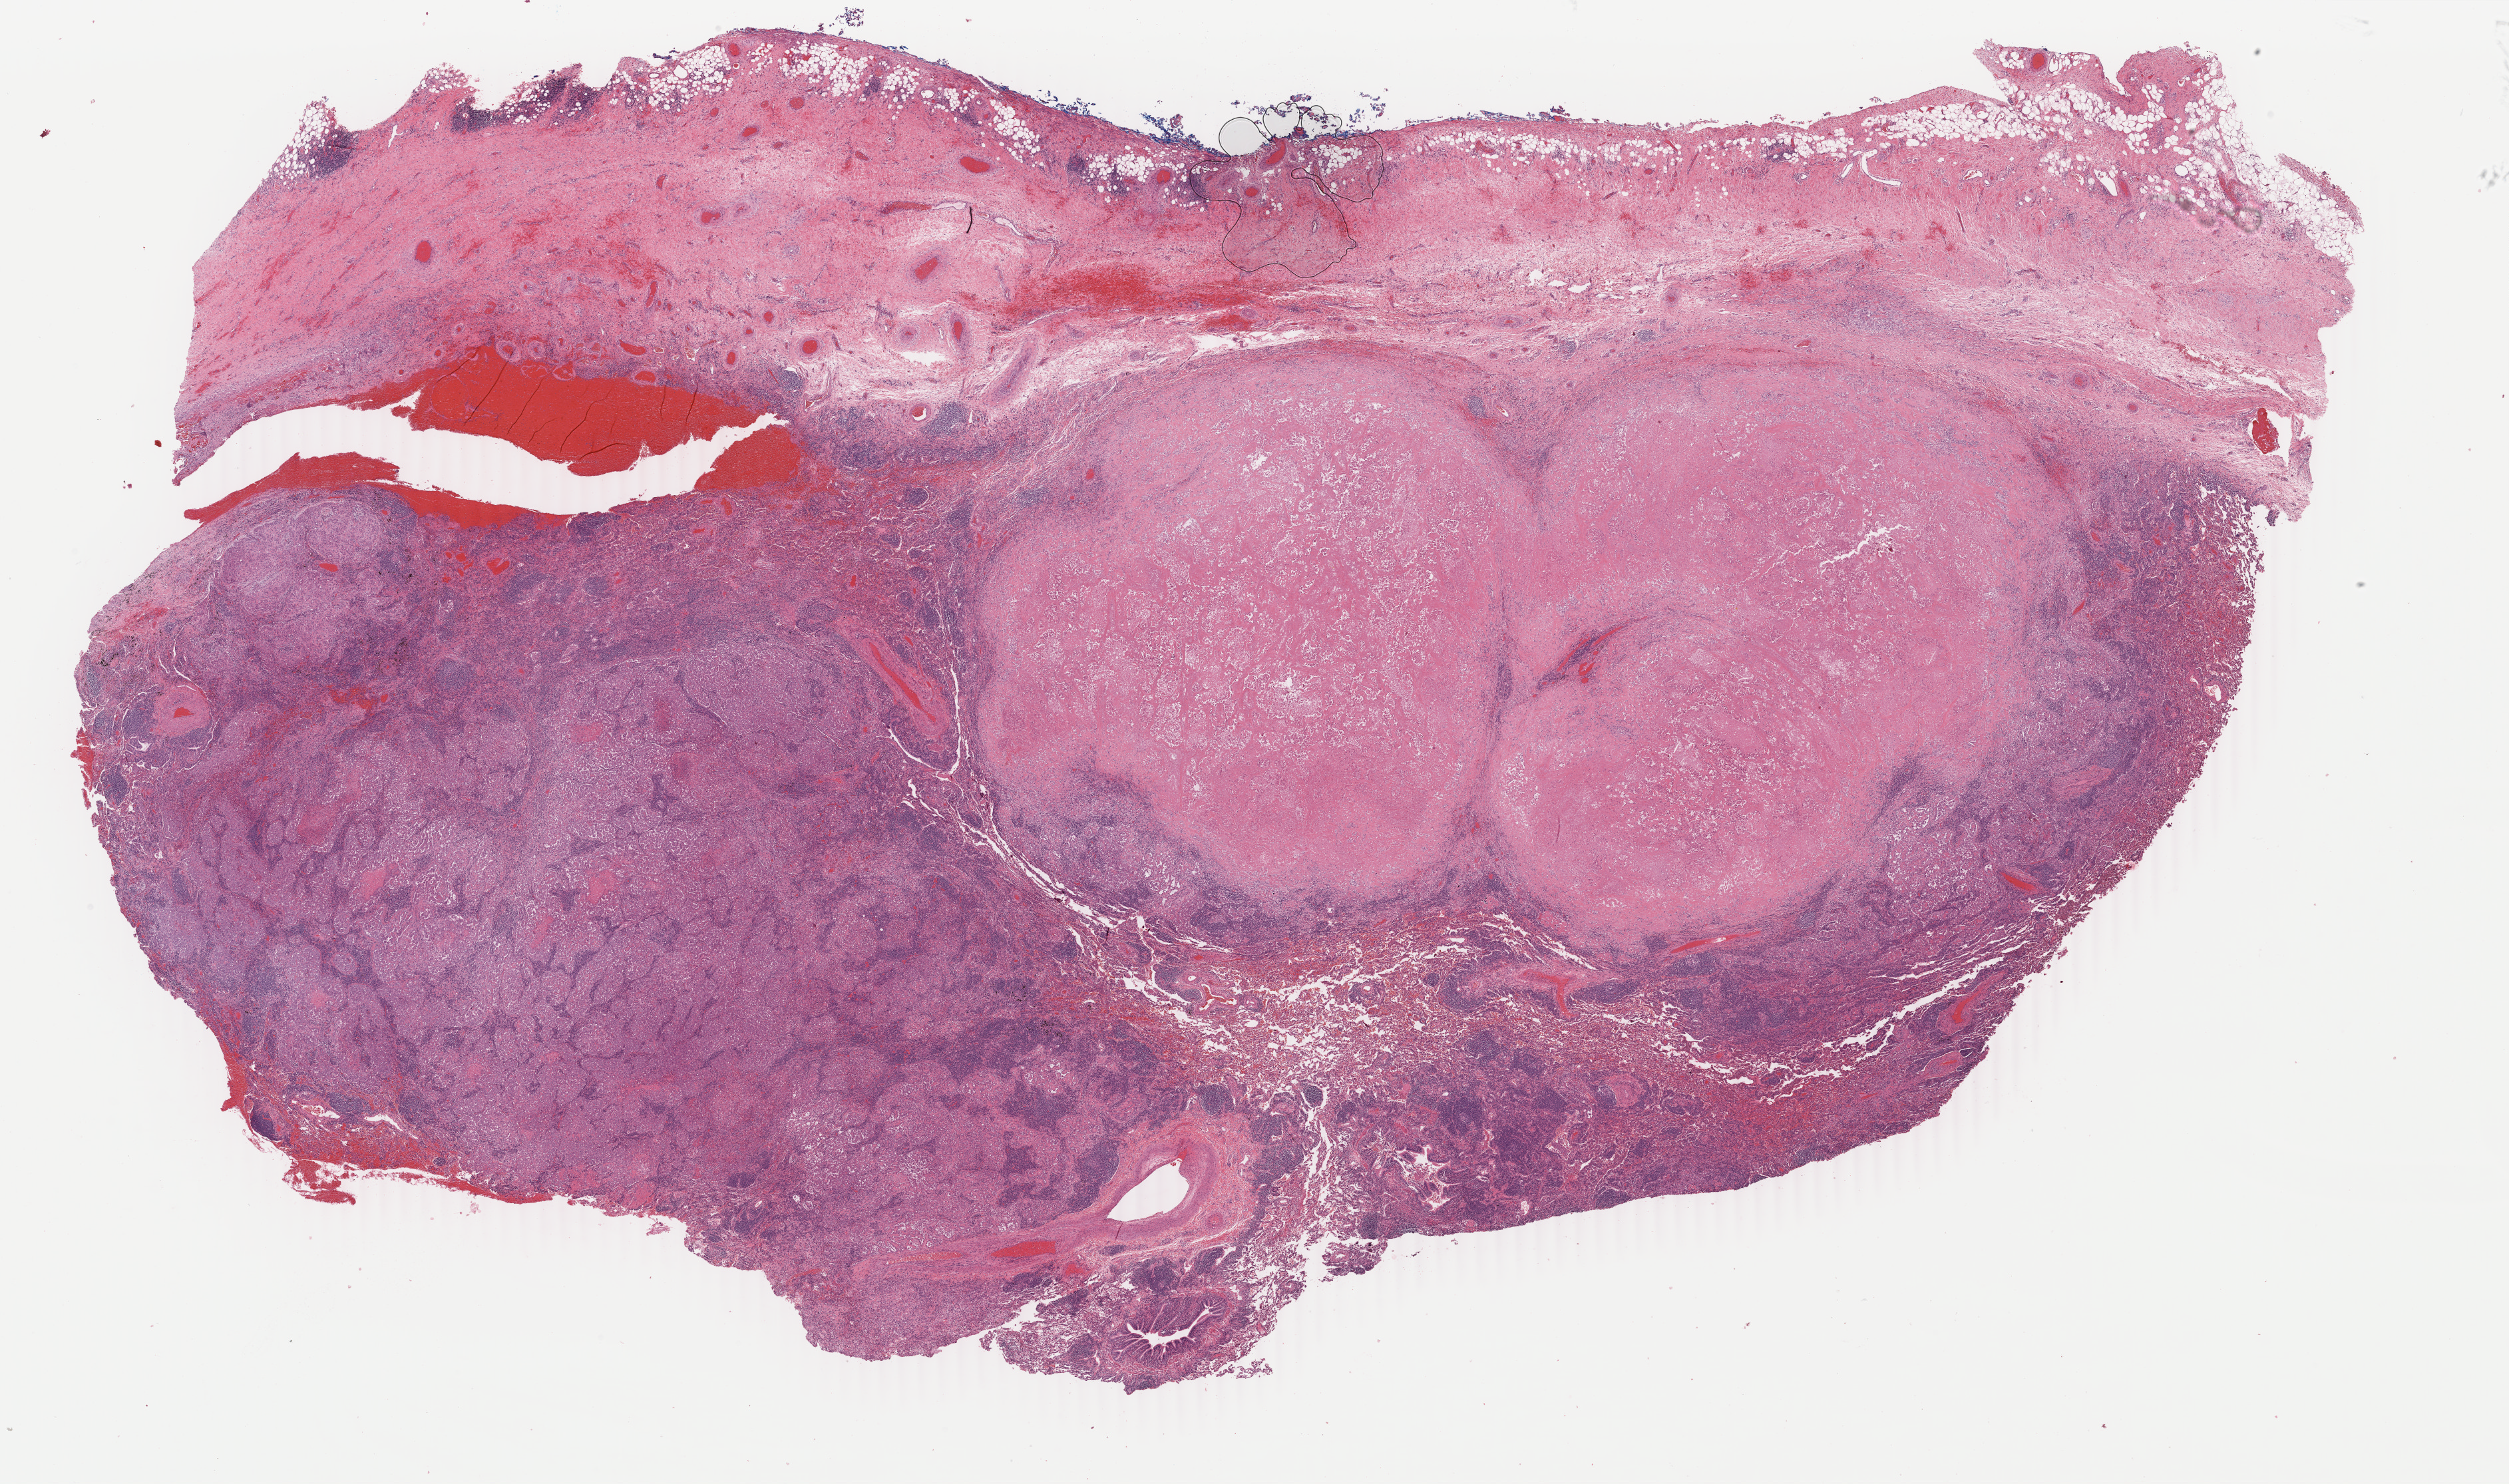
H&E-stained whole-slide image — low-resolution overview of the scanned area, about 30.0 x 17.7 mm (acquisition: 40x scan). Formalin-fixed paraffin-embedded (FFPE) diagnostic section. Mesothelium, primary tumour sample. Male patient; age at initial diagnosis 69 years.
TNM: T2 N1 M0. Diagnosis: Epithelioid mesothelioma, malignant (pleura, NOS). Laterality: left. AJCC pathologic stage: III (6th edition).